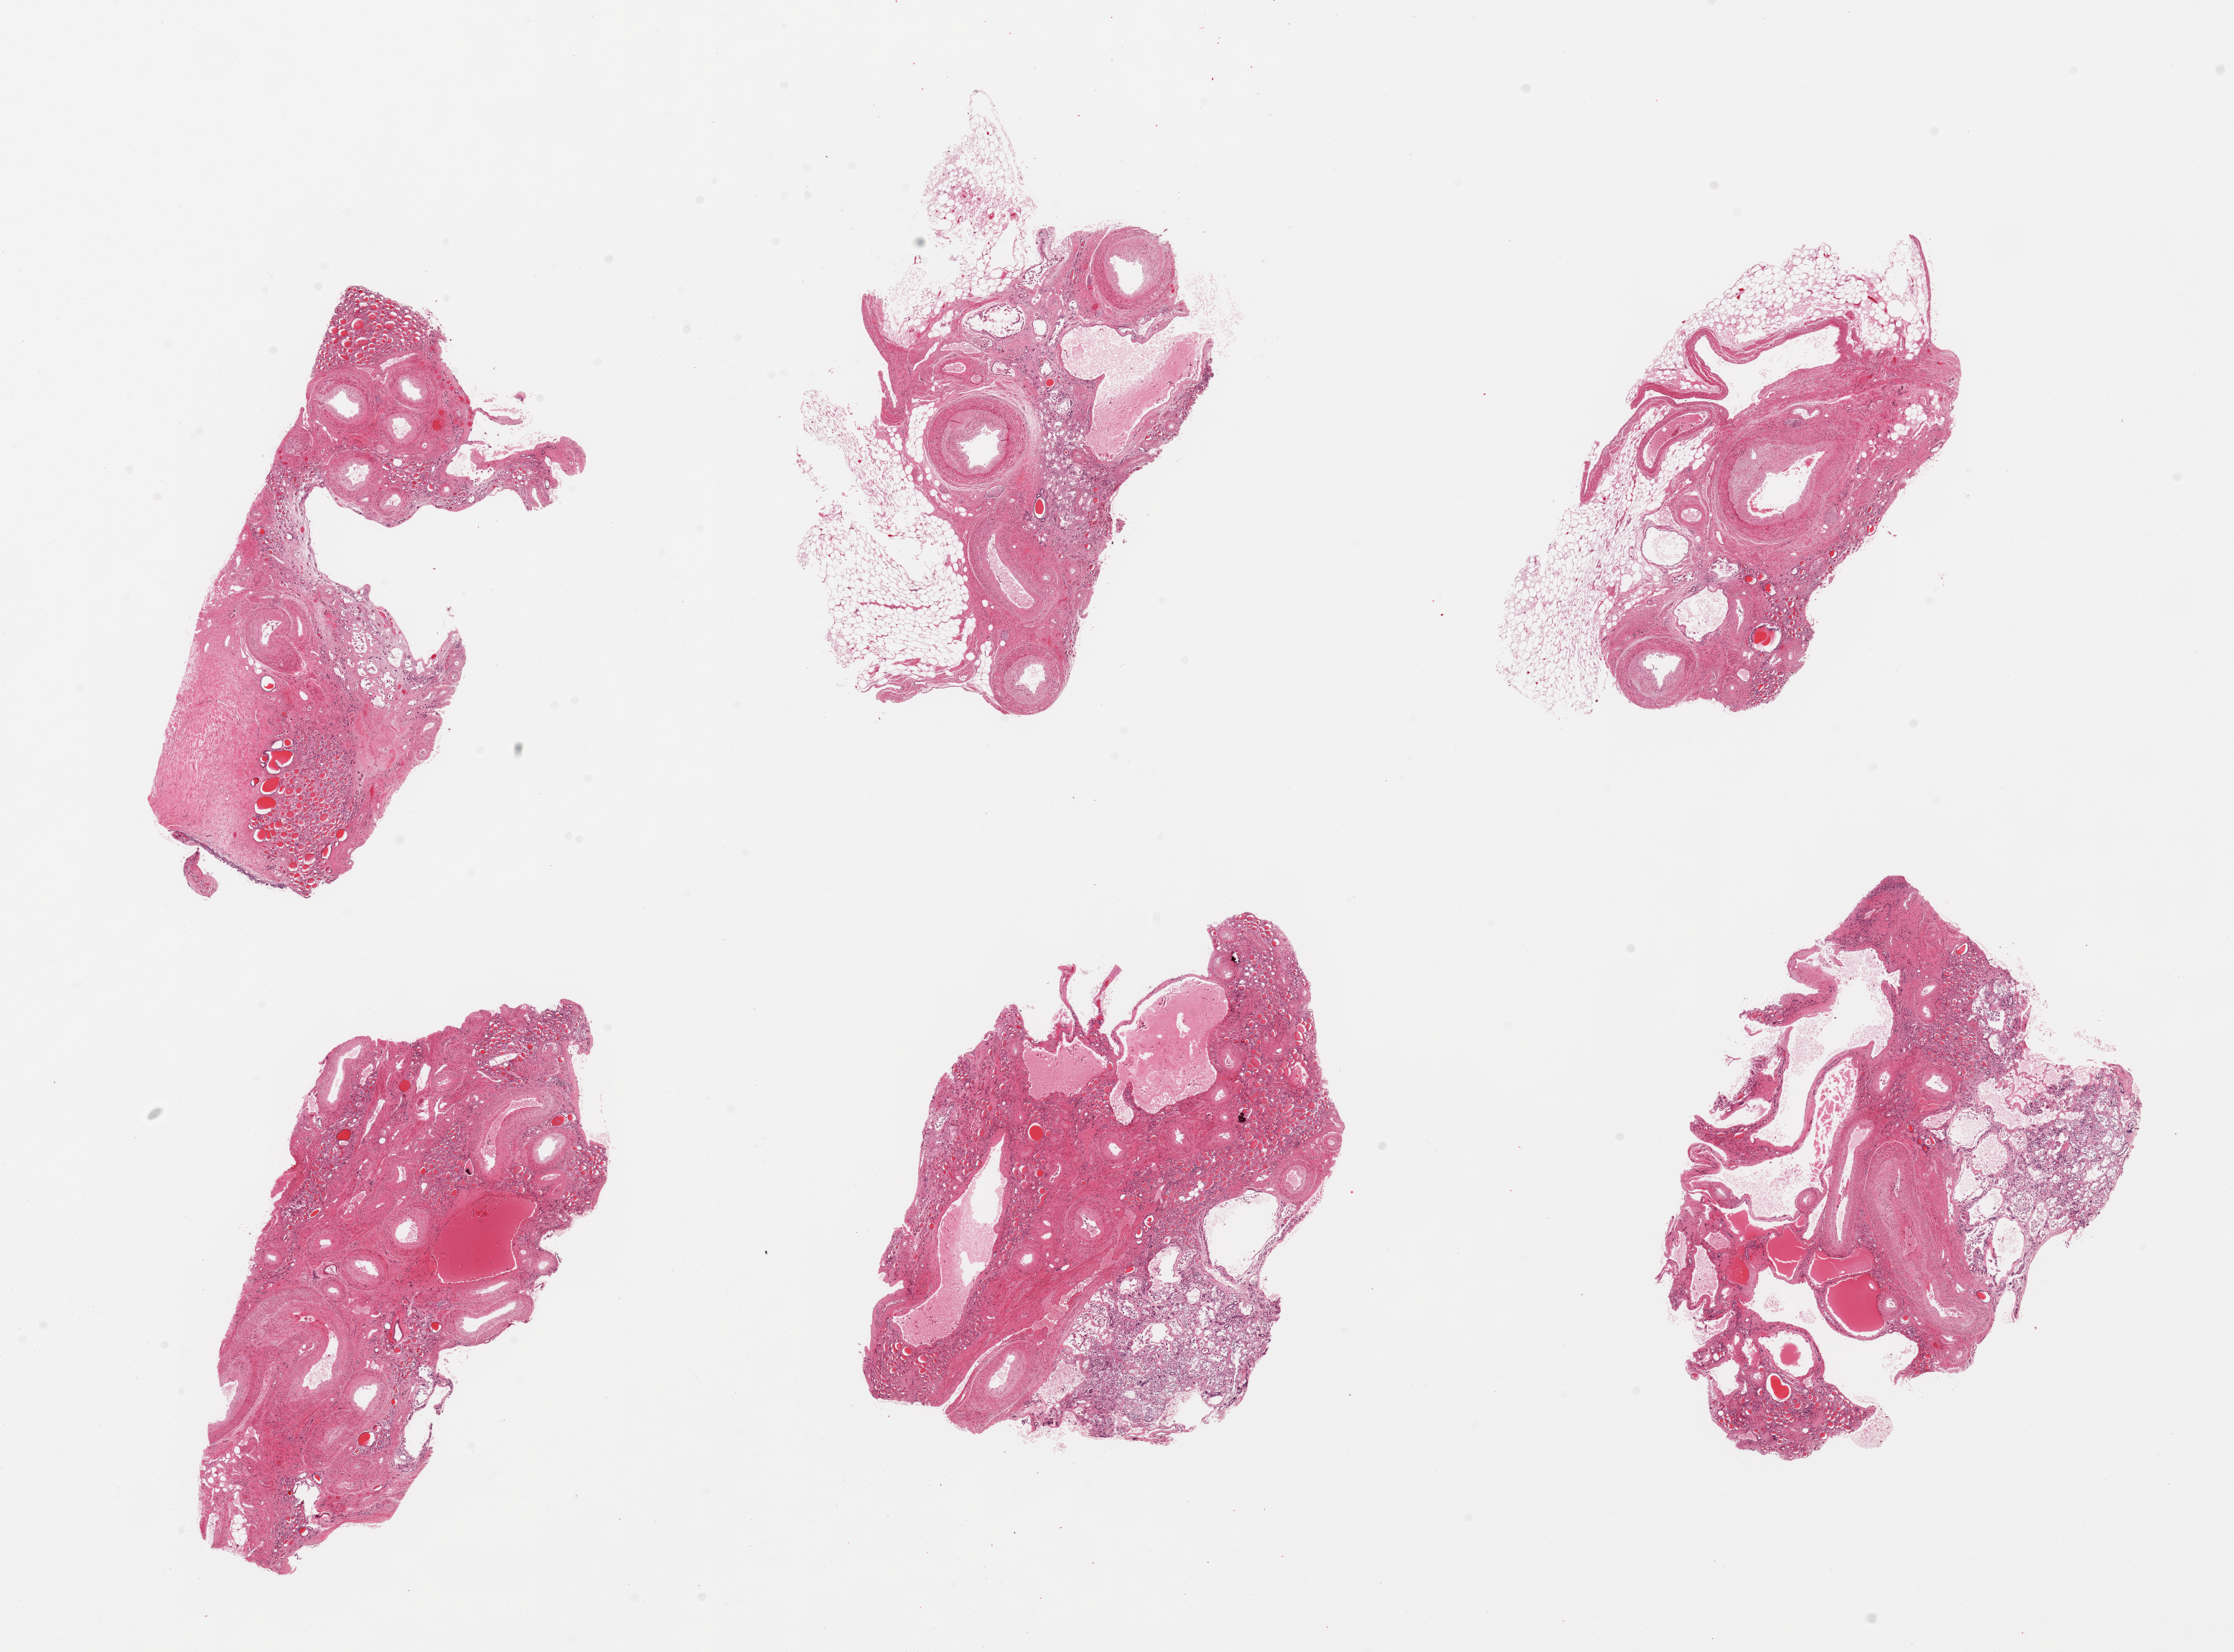
Haematoxylin and eosin whole-slide image, brightfield, a low-resolution overview of the entire scanned area, about 24.6 x 18.2 mm (slide scanned at 20x). PAXgene-fixed paraffin-embedded (PFPE) section. Target tissue: renal cortex. Donor tissue sample.
Reviewer comment on this tissue sample: 6 pieces, mainly fat/vasuclar tissue, endstage nephritis/dystrophic appearing in trace residual kidney.